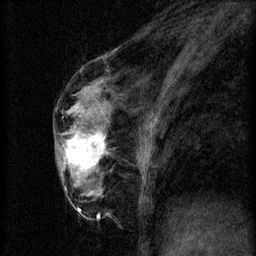
Breast MRI (dynamic contrast-enhanced), one sagittal slice. Position 27 of 60 along the scan axis. 3 images stored at this slice position (order not interpretable as contrast timing). 1.5 T. TE 4.2 ms, TR 8.2 ms. 256 × 256 image matrix, field of view 180 × 180 mm. Female patient, age 56 years.
Structures marked on this image (semi-automatic segmentation, software-assisted and operator-edited):
- analysis volume of interest (the breast-tissue region the enhancement analysis was run in; not a lesion): bounding box <60,124,111,179> (left, top, right, bottom; pixels)
- tumour enhancement mask (voxels above the 70 % enhancement threshold inside the analysis volume of interest): <64,132,105,171>